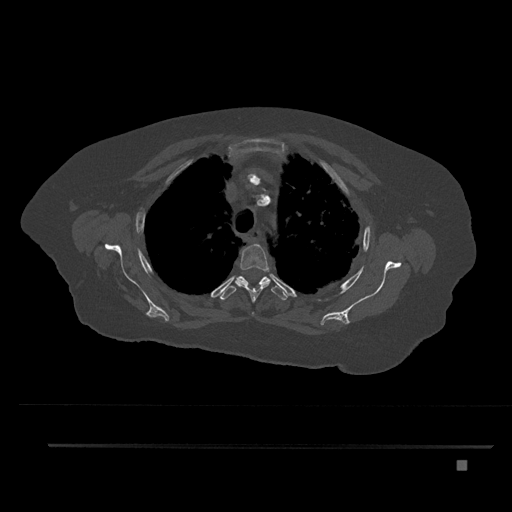
CT including the spine, one axial slice. Position 623 of 797 along the scan axis. Reconstruction kernel Br40s/3. 120 kVp. Bone window (W 1800 / L 400 HU). 0.5 mm slice thickness. 512 × 512 image matrix, field of view 437 × 437 mm. Female patient, age 76 years. From the clinical record (not read from this slice): primary cancer: lung; vertebrae with lytic lesions (as recorded): T11, L3.
Structures marked on this image (semi-automatically segmented with operator editing):
- T3 vertebra: bounding box [x1, y1, x2, y2] px = [235, 243, 270, 315]
- T4 vertebra: [219, 276, 288, 300]